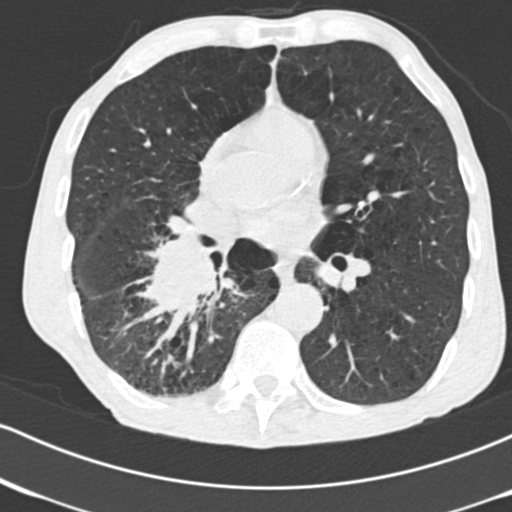
Low-dose screening chest CT, one axial slice; slice 83 of 182 in the series (ordered by position); 120 kVp; lung window (W 1500 / L -600 HU); 512 × 512 image matrix.
Outlined on this slice (expert manual segmentation):
- lesion 1 (tumor, lower lobe of right lung): bounding box [x1, y1, x2, y2] px = [146, 242, 220, 317]